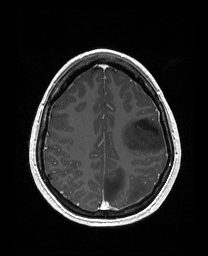
Brain MRI from a brain-tumour surgery series, one axial slice; slice 117 of 176 in the series (ordered by position); T1-weighted post-contrast; 1 mm slice thickness; 208 × 256 image matrix. Case-level facts recorded for this patient, not image findings: histopathology: Astrocytoma; WHO grade: 3; IDH mutation: yes; tumour location: Left Frontal.
Outlined on this slice (outlined manually by an expert reader):
- tumour: box from (x=121, y=117) to (x=165, y=153) px